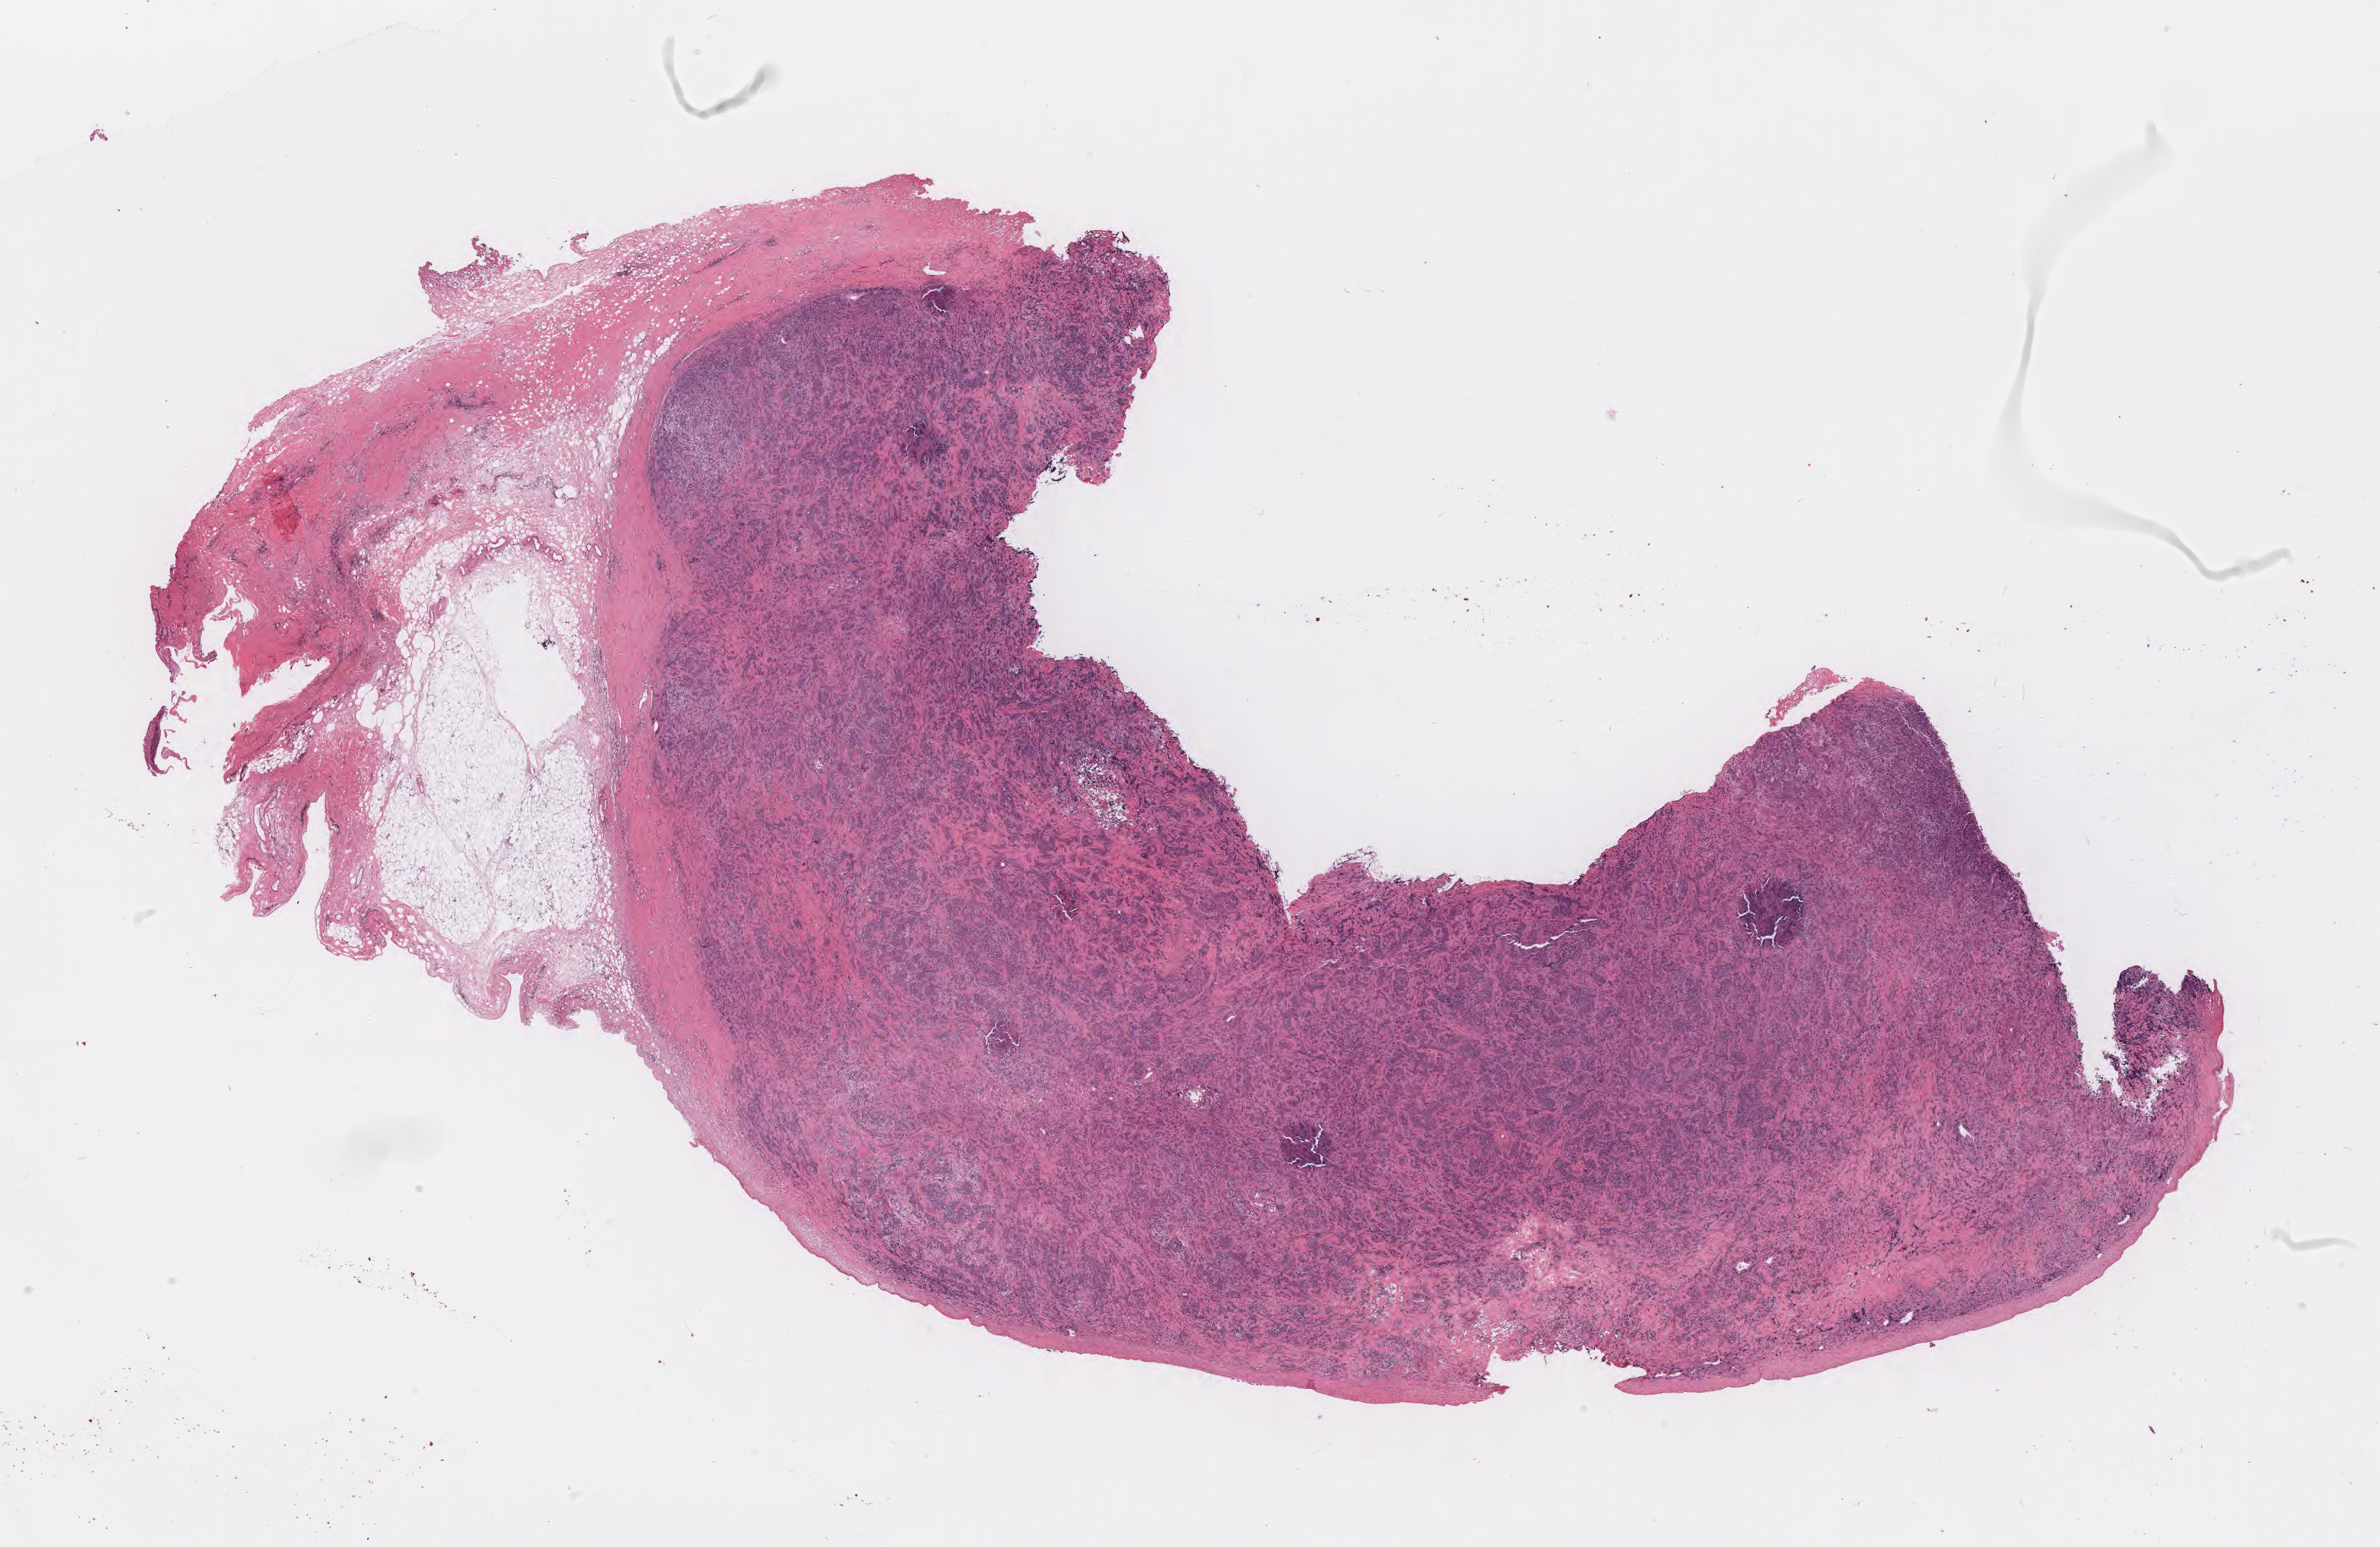
Whole-slide image, hematoxylin and eosin (H&E) stain — low-resolution overview of the scanned area, about 26.7 x 17.3 mm, specimen: tumor tissue, site: bone. Patient male; 48 years old.
* histologic diagnosis: Diffuse large B-cell lymphoma, NOS